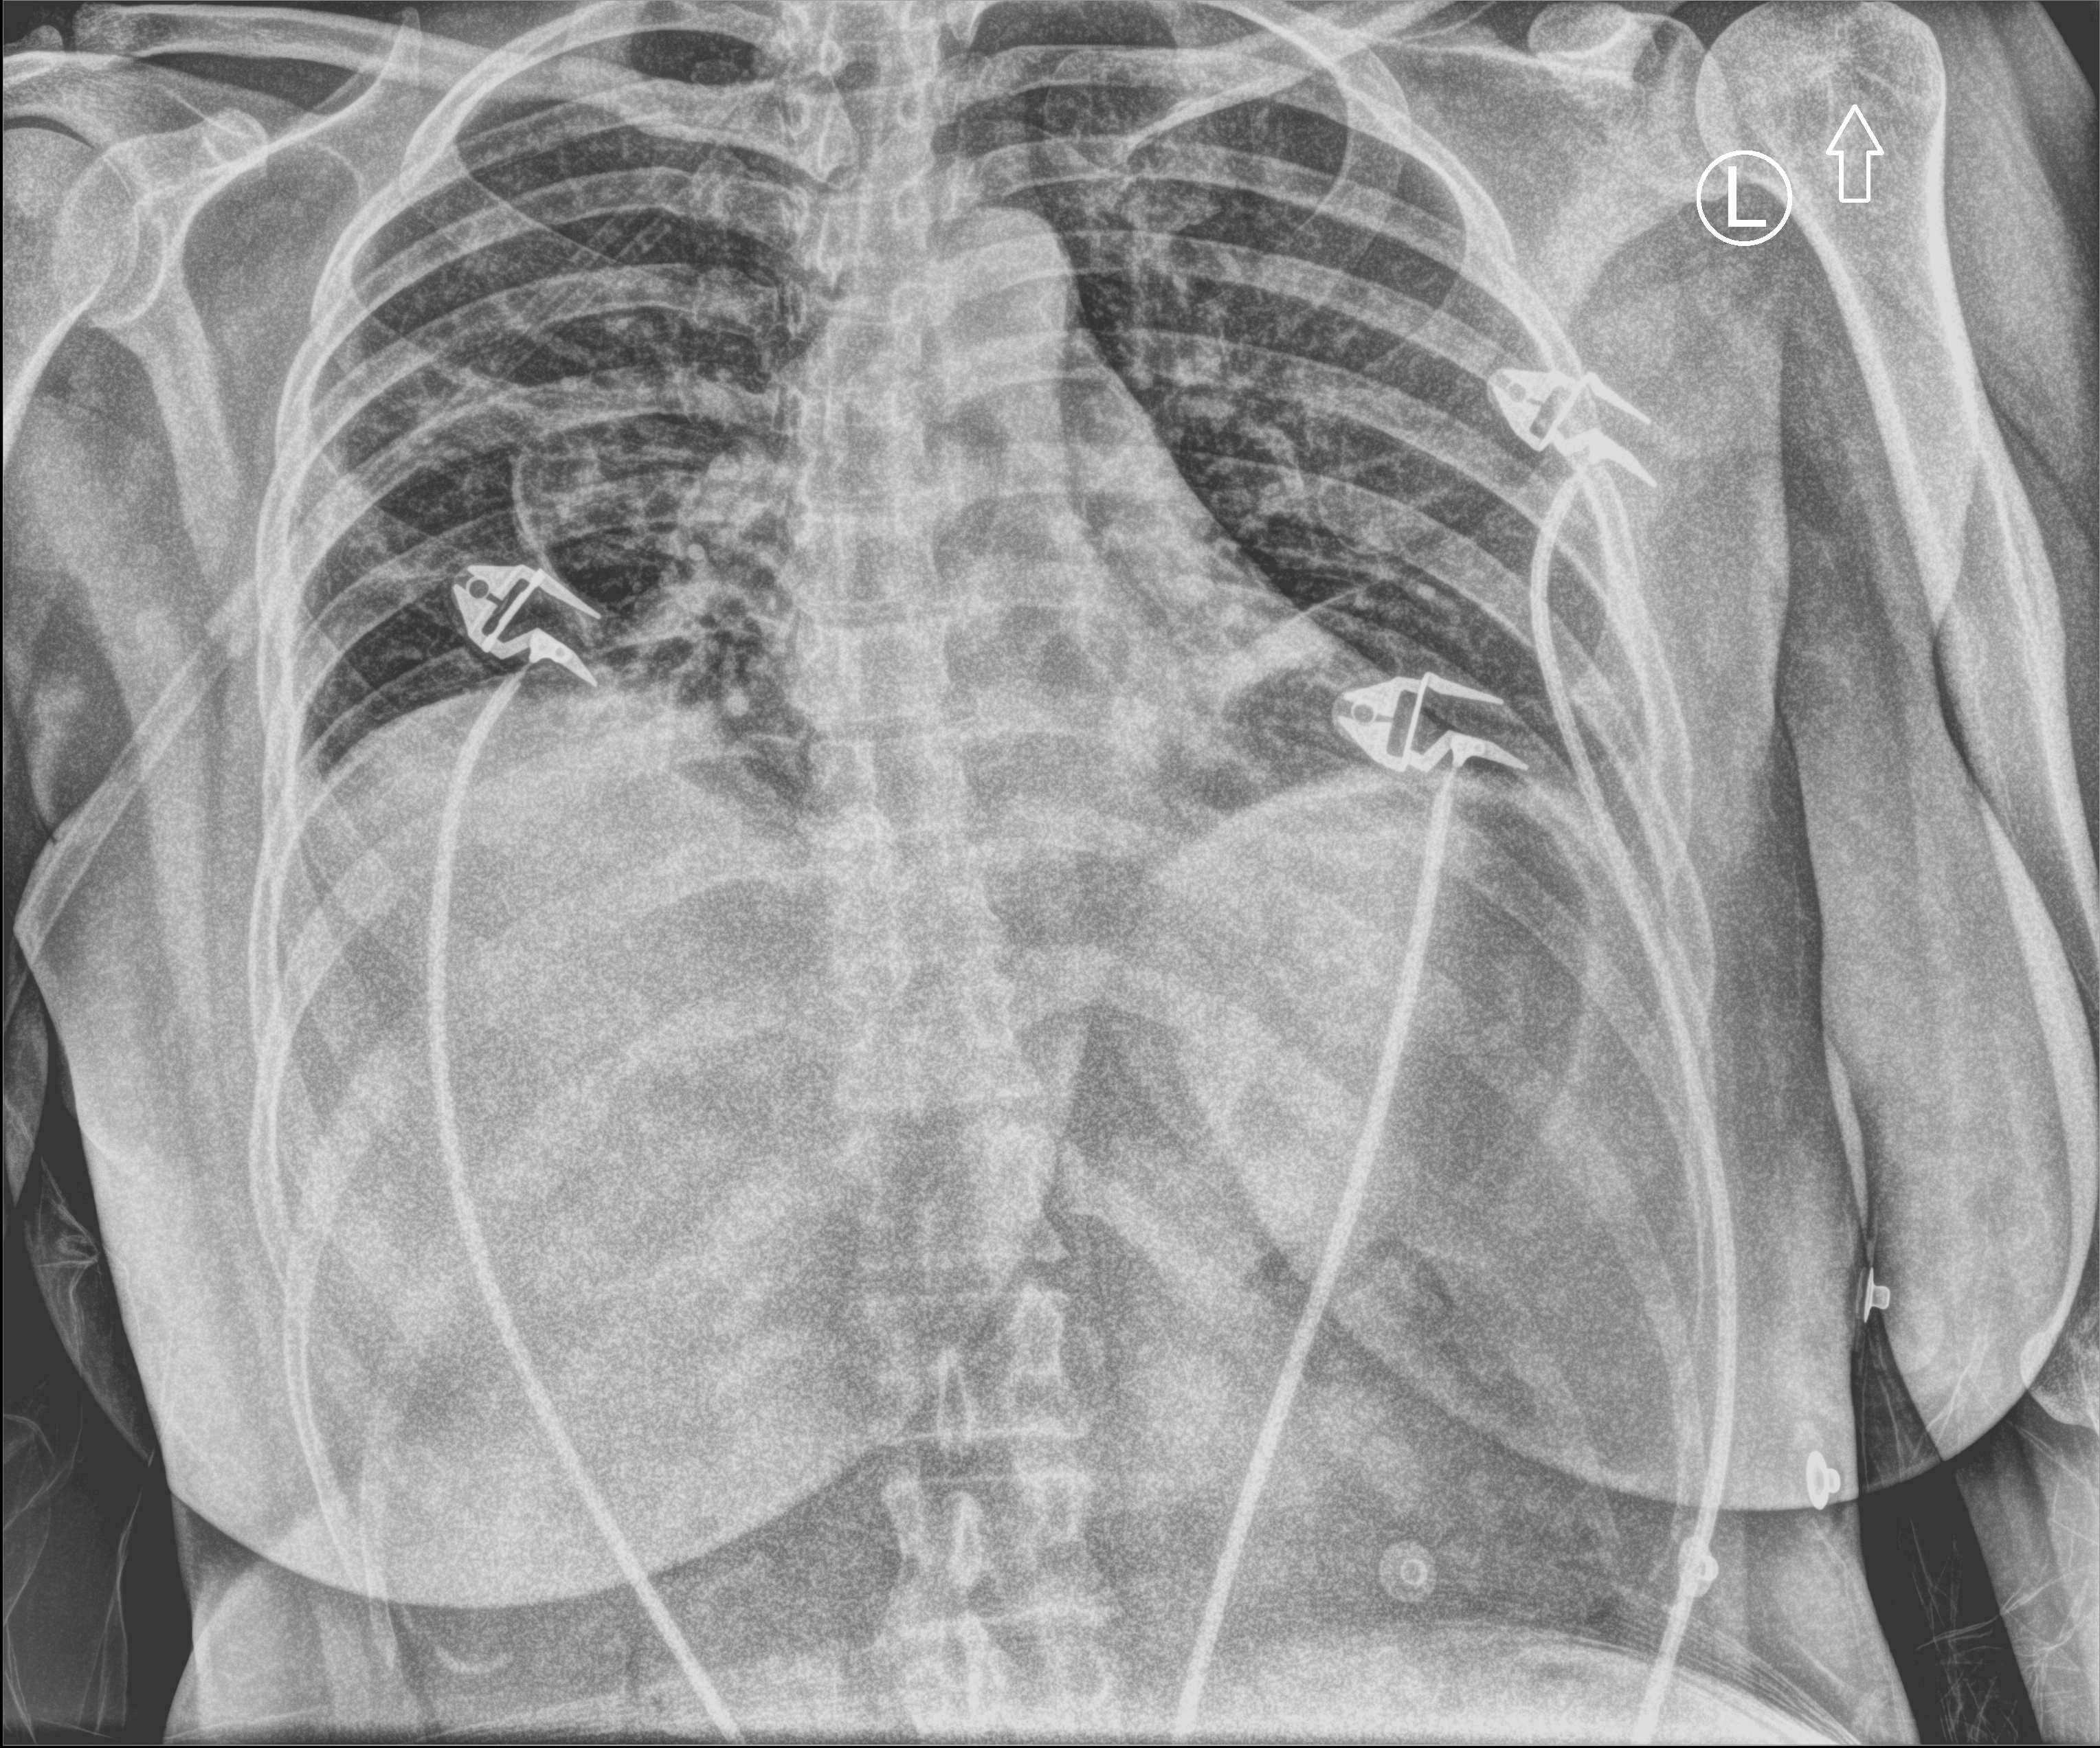
Bedside chest radiograph (computed radiography). Patient hospitalised with COVID-19; female, aged 18–59 years.
Hospital-stay facts (about this admission, not read from this image; timing relative to this image not recorded): admitted to intensive care during this hospital stay: no.